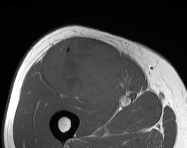
MRI of an extremity soft-tissue mass, one axial slice. Position 80 of 114 along the scan axis. MR volume resampled by the dataset authors to the PET/CT grid (not the native acquisition matrix). 3.27 mm slice thickness. 187 × 148 image matrix. Male patient. Case-level facts recorded for this patient, not image findings: histological type: pleiomorphic leiomyosarcoma; grade: intermediate; site of the primary tumour: right thigh.
Outlined on this slice (expert contour drawn on MRI and transferred to this co-registered scan by the dataset authors):
- gross tumour volume including surrounding oedema: bounding box <45,38,131,101> (left, top, right, bottom; pixels)
- gross tumour volume (mass): <45,38,131,101>